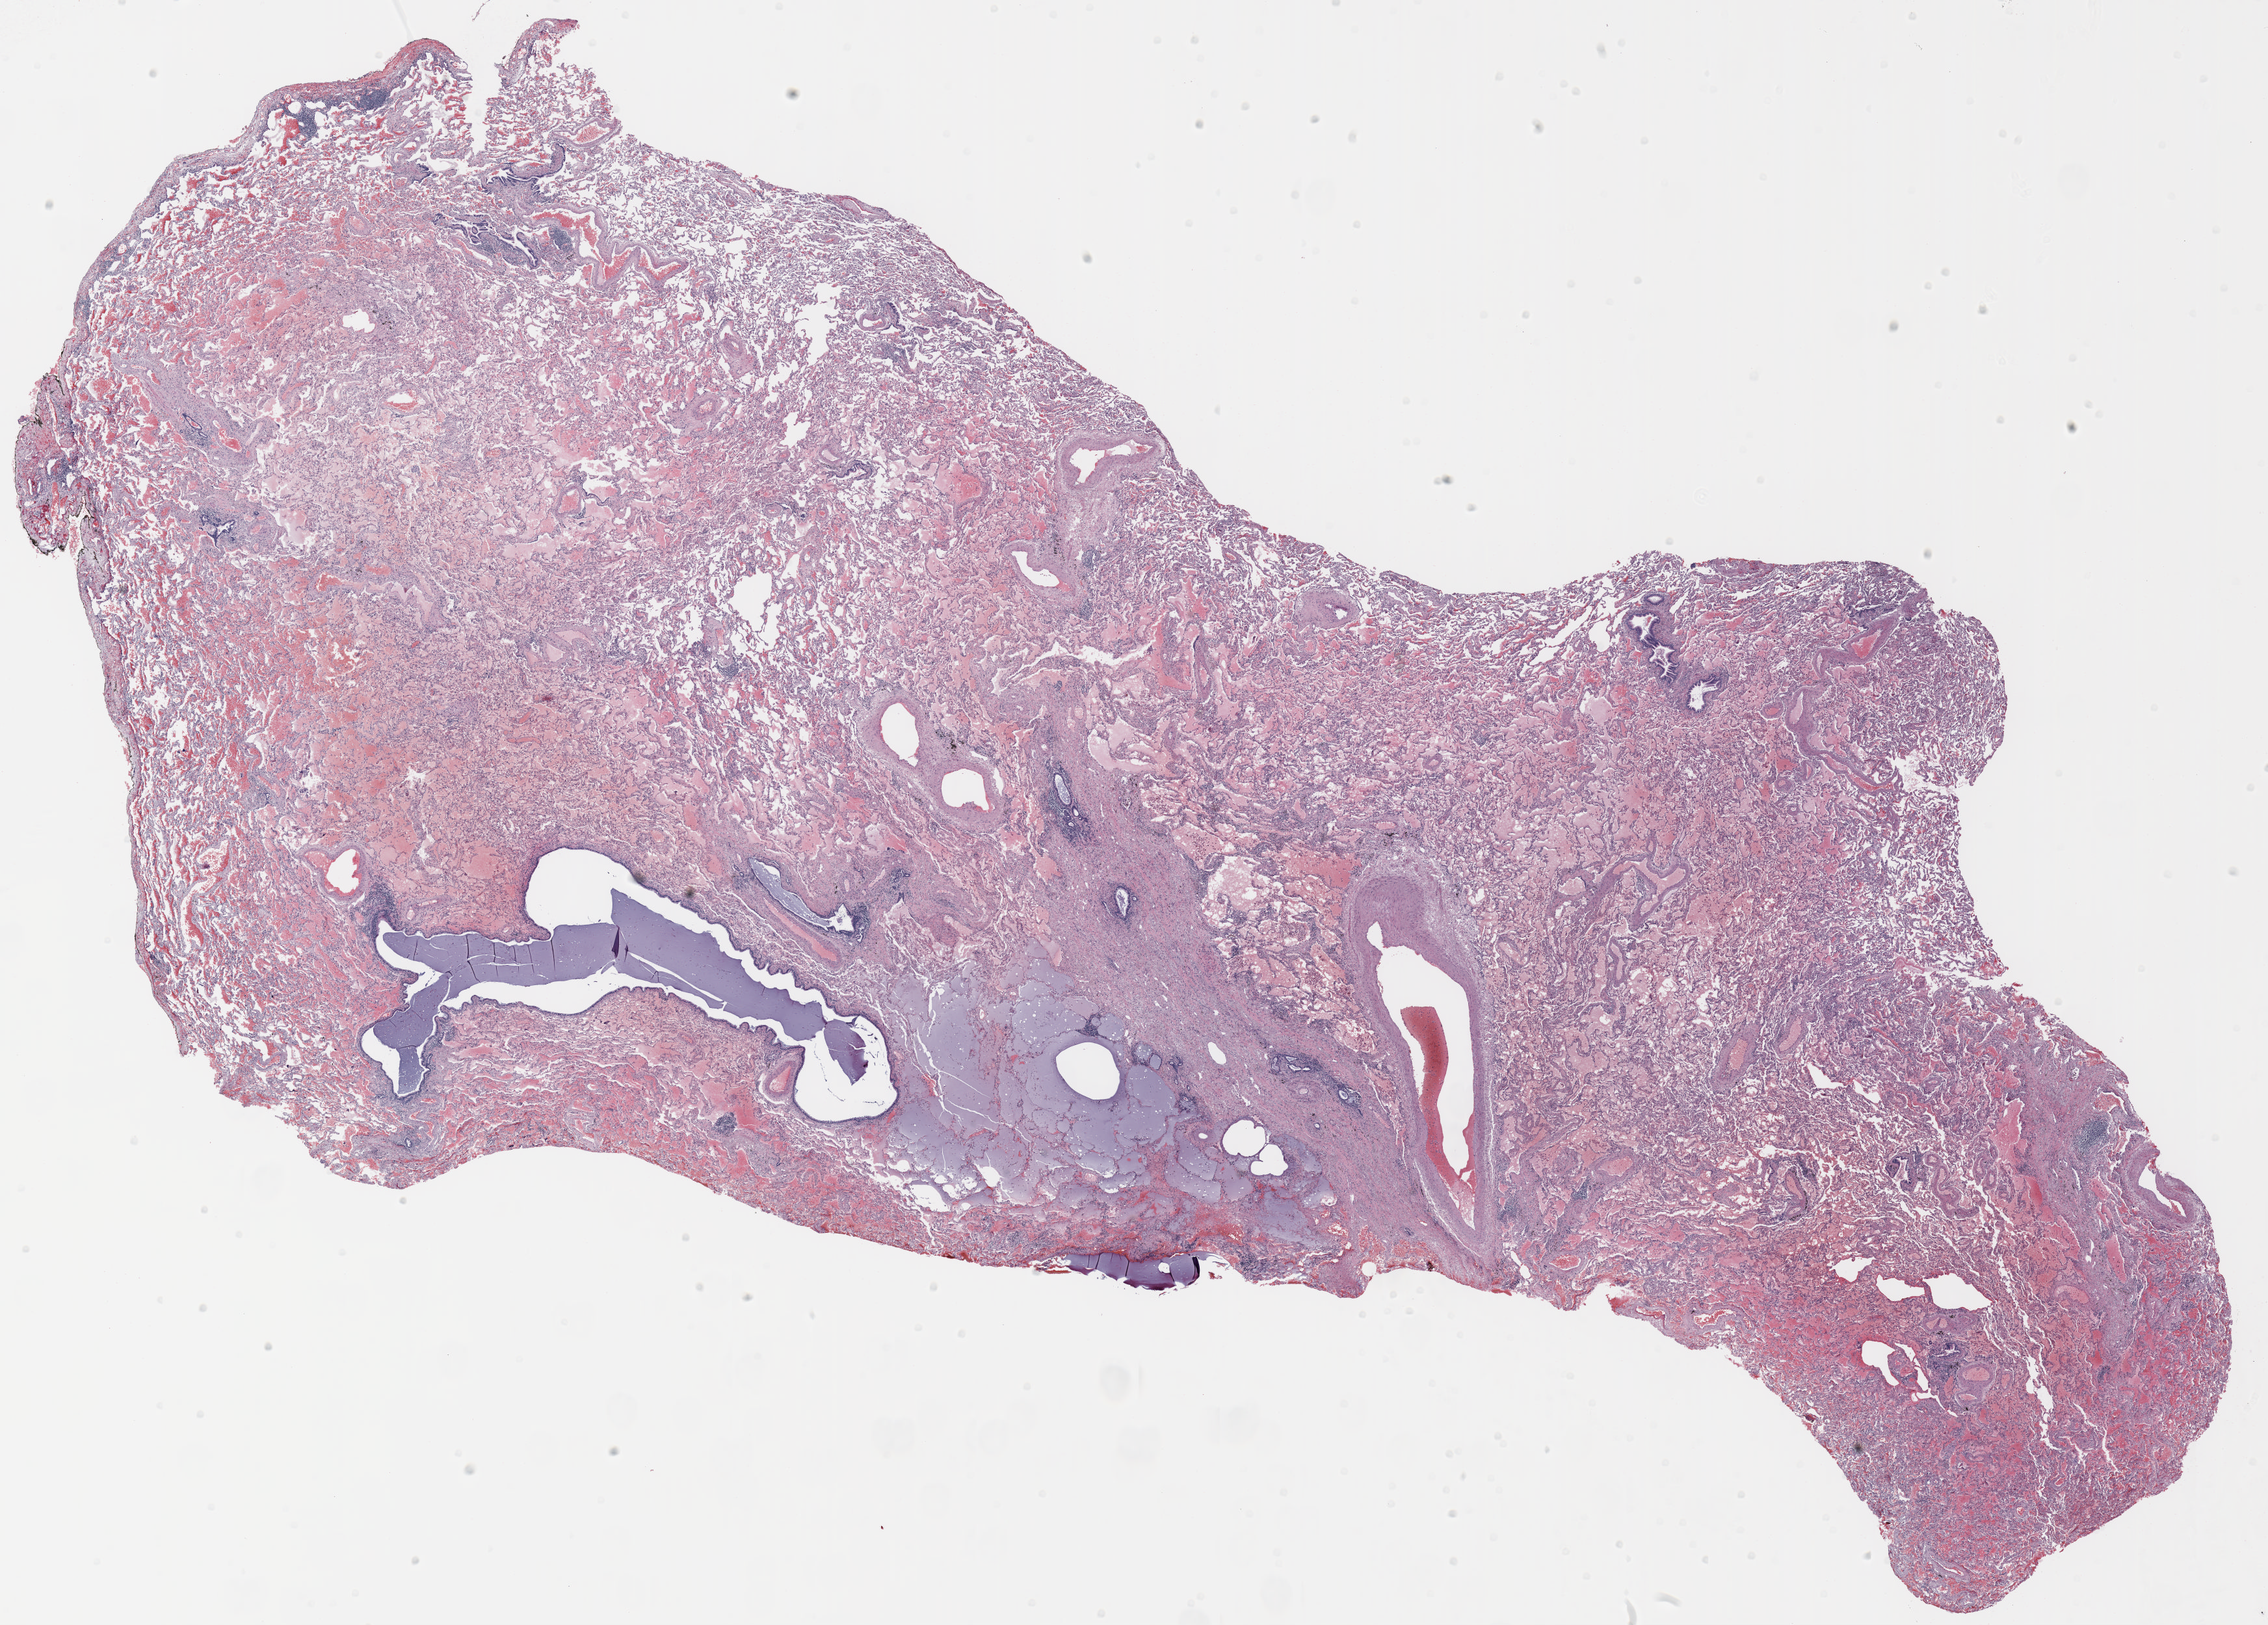
Hematoxylin and eosin (H&E) stained whole-slide image, whole scanned area (about 28.0 x 20.1 mm, from a 20x scan) shown as a low-resolution overview. FFPE section. Lung tissue. Male, age 73 at enrolment.
Participant's lung-cancer diagnosis: Carcinoid tumor, NOS.